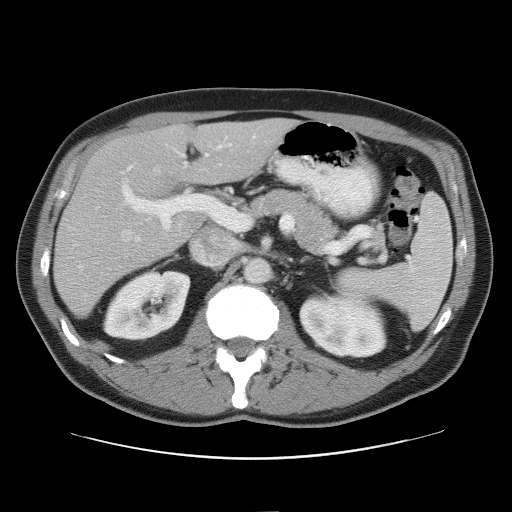
Contrast-enhanced abdominal CT, one axial slice; slice 33 of 52 in the series (ordered by position); reconstruction kernel STANDARD; soft-tissue window (W 400 / L 40 HU); 5 mm slice thickness; 512 × 512 image matrix, field of view 393 × 393 mm. Male patient, age 70 years. Case-level facts recorded for this patient, not image findings: diagnosis: colorectal cancer liver metastases, imaged before liver resection.
Structures marked on this image (outlined manually by an expert reader):
- hepatic veins: bounding box (x1, y1, x2, y2) in pixels: (74, 168, 160, 270)
- liver: (56, 121, 293, 316)
- planned liver remnant (the part of the liver to remain after resection): (110, 121, 293, 185)
- portal vein (with intrahepatic branches): (122, 143, 231, 231)